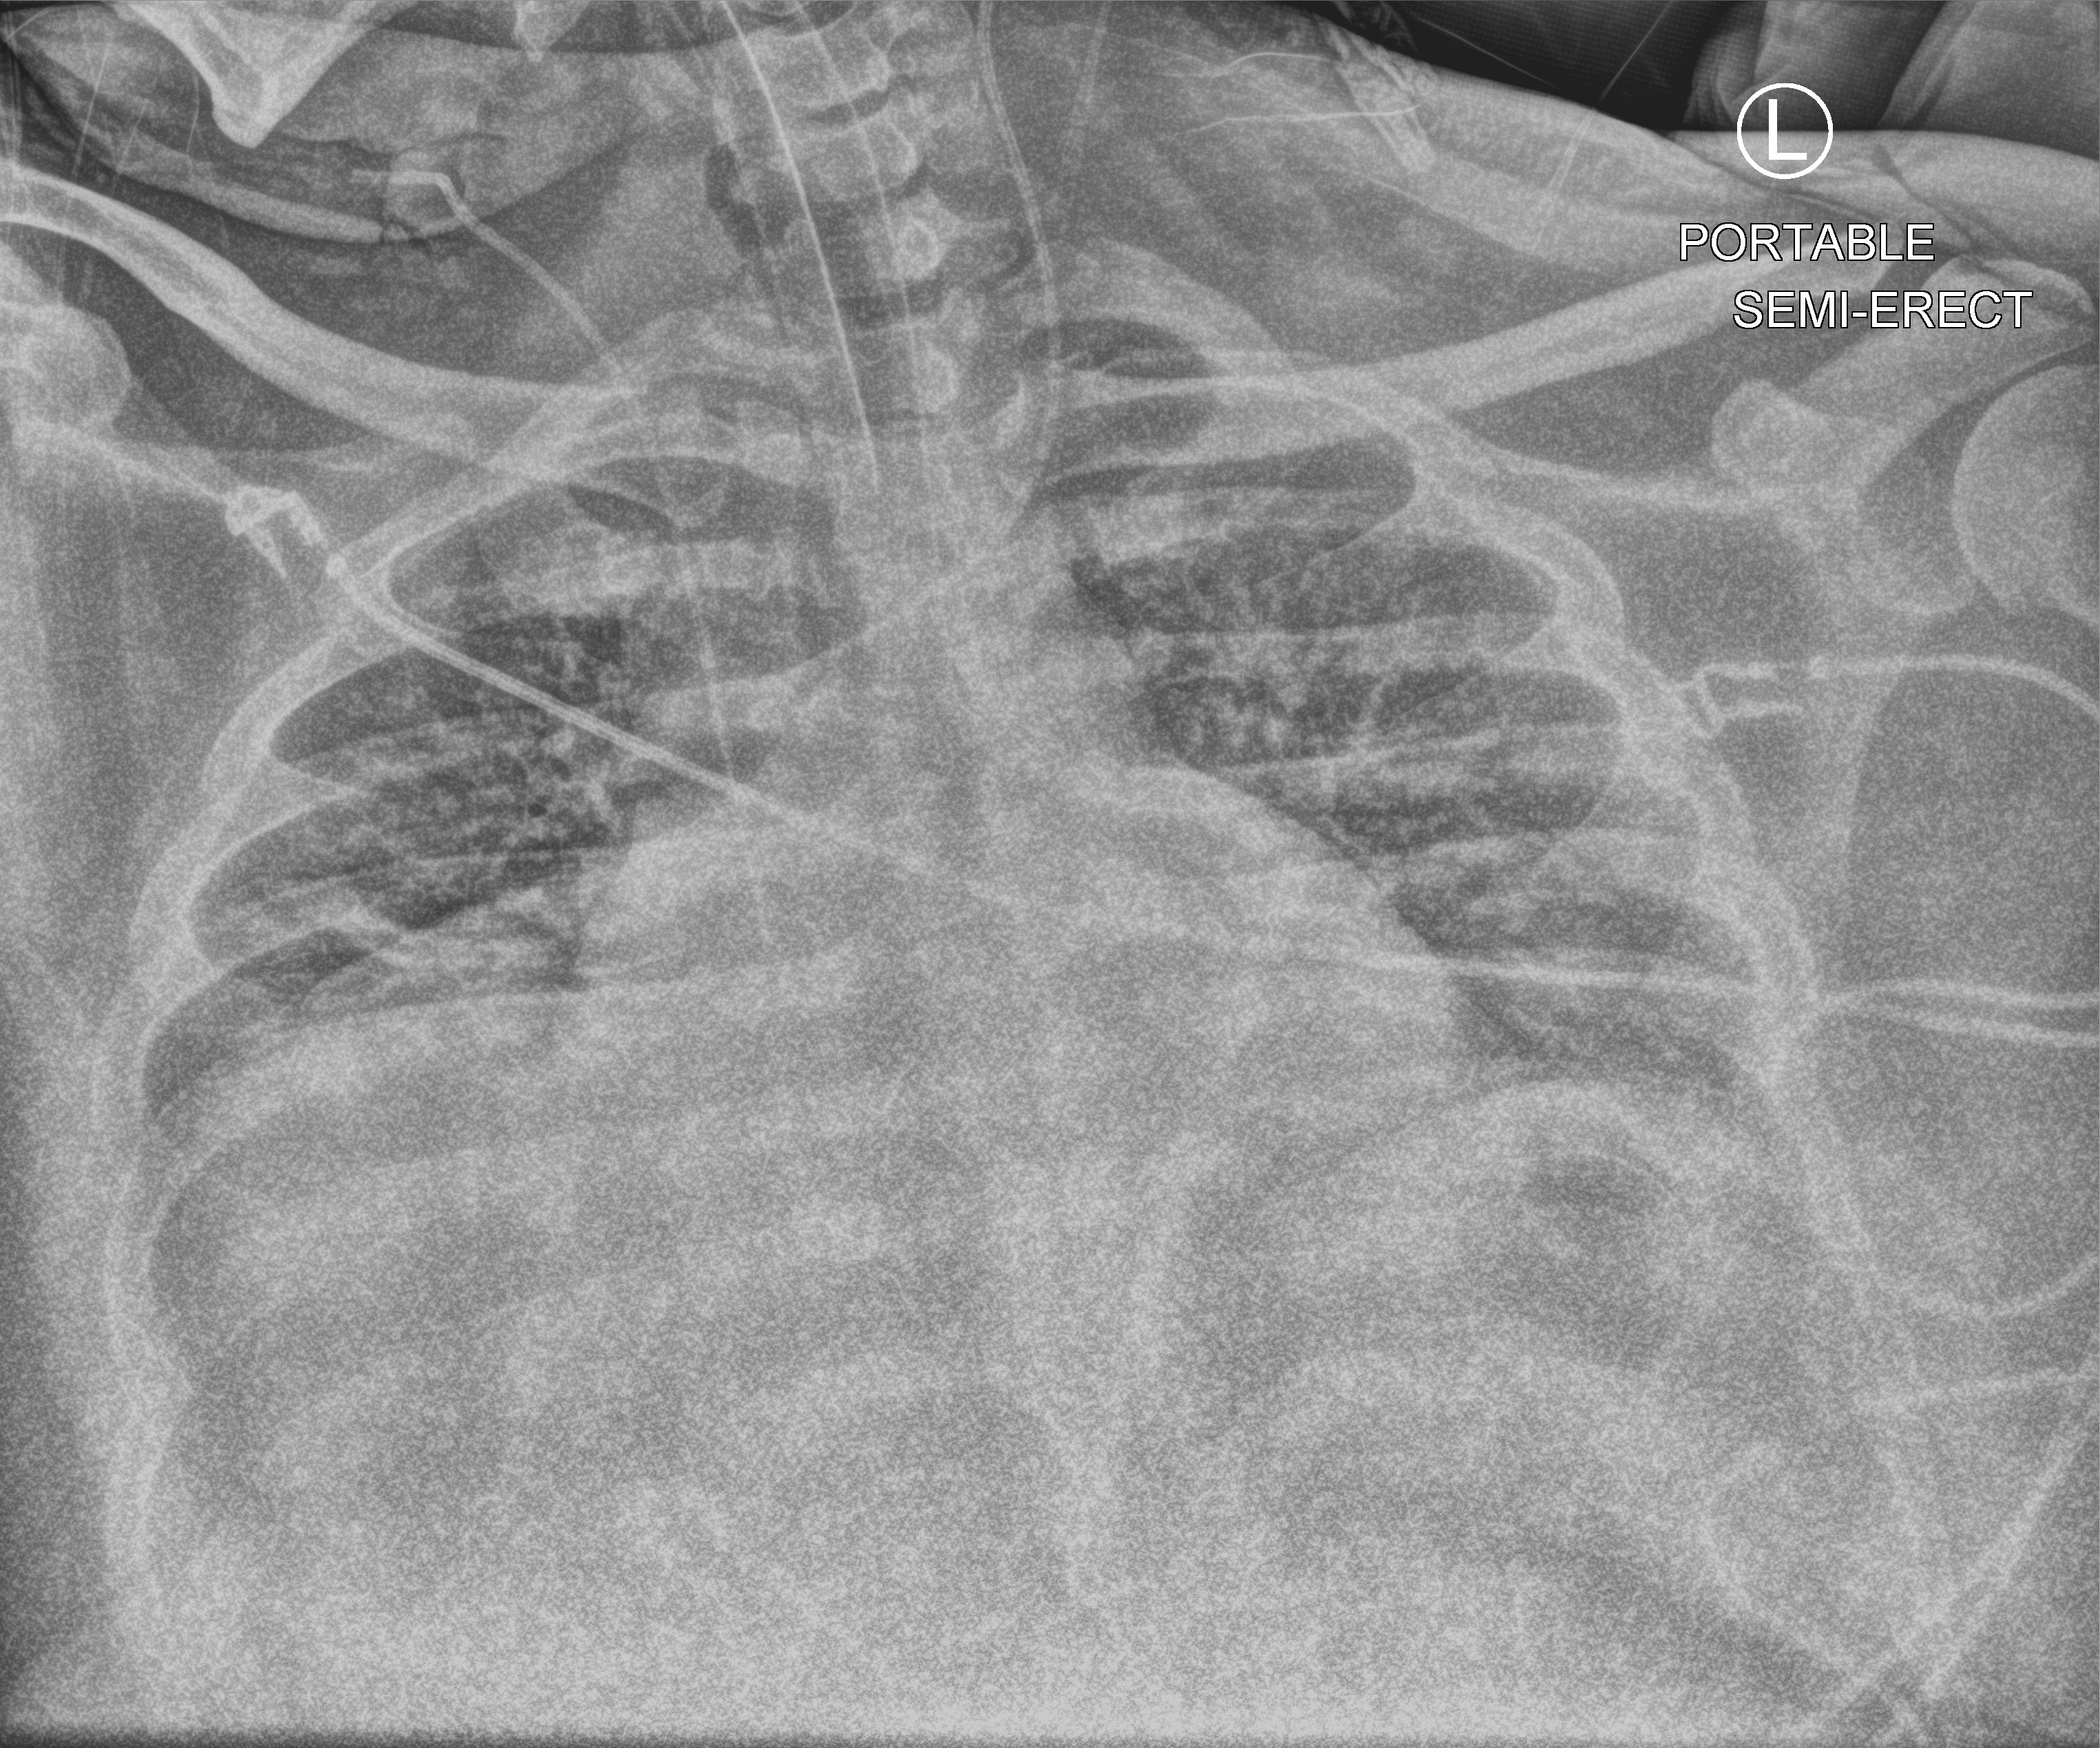
Bedside chest radiograph (computed radiography); anteroposterior (AP) projection. Male patient hospitalised with COVID-19, age 18–59 years.
Admission-level facts for this patient (not findings on this image; timing relative to this image not recorded):
- mechanically ventilated during this hospital stay: yes
- admitted to intensive care during this hospital stay: yes
- hypertension (admission record): no